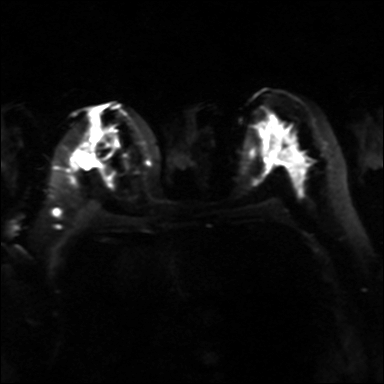
Breast MRI, one axial slice. Diffusion-weighted series; image 2 of 4 stored at this slice position (different b-values; order by instance number). 3 T. 384 × 384 image matrix, field of view 320 × 320 mm. Female patient.
Outlined on this slice (expert manual segmentation):
- tumour on diffusion-weighted imaging: box from (x=73, y=152) to (x=97, y=167) px